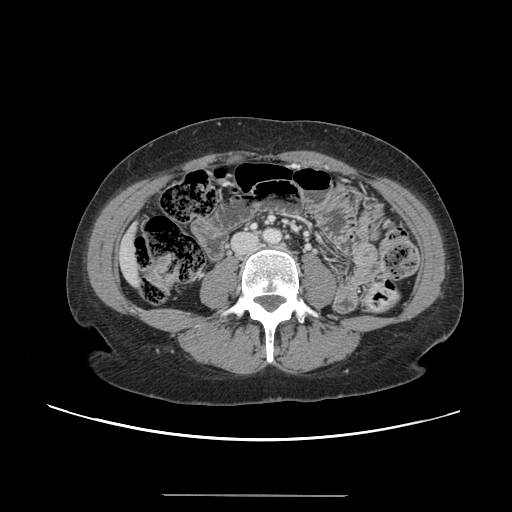
Contrast-enhanced abdominal CT, one axial slice; position 17 of 144 along the scan axis; 120 kVp; intravenous contrast given; soft-tissue window (W 400 / L 40 HU); 512 × 512 image matrix, field of view 380 × 380 mm. Female patient, age 53 years. From the clinical record (not read from this slice): diagnosis: colorectal cancer liver metastases, imaged before liver resection; multiple liver metastases: yes; largest metastasis: 1.1 cm; disease in both lobes: no.
Annotated regions visible in this slice (expert manual segmentation):
- liver: bounding box (x1, y1, x2, y2) in pixels: (119, 227, 140, 287)
- planned liver remnant (the part of the liver to remain after resection): (117, 227, 140, 288)